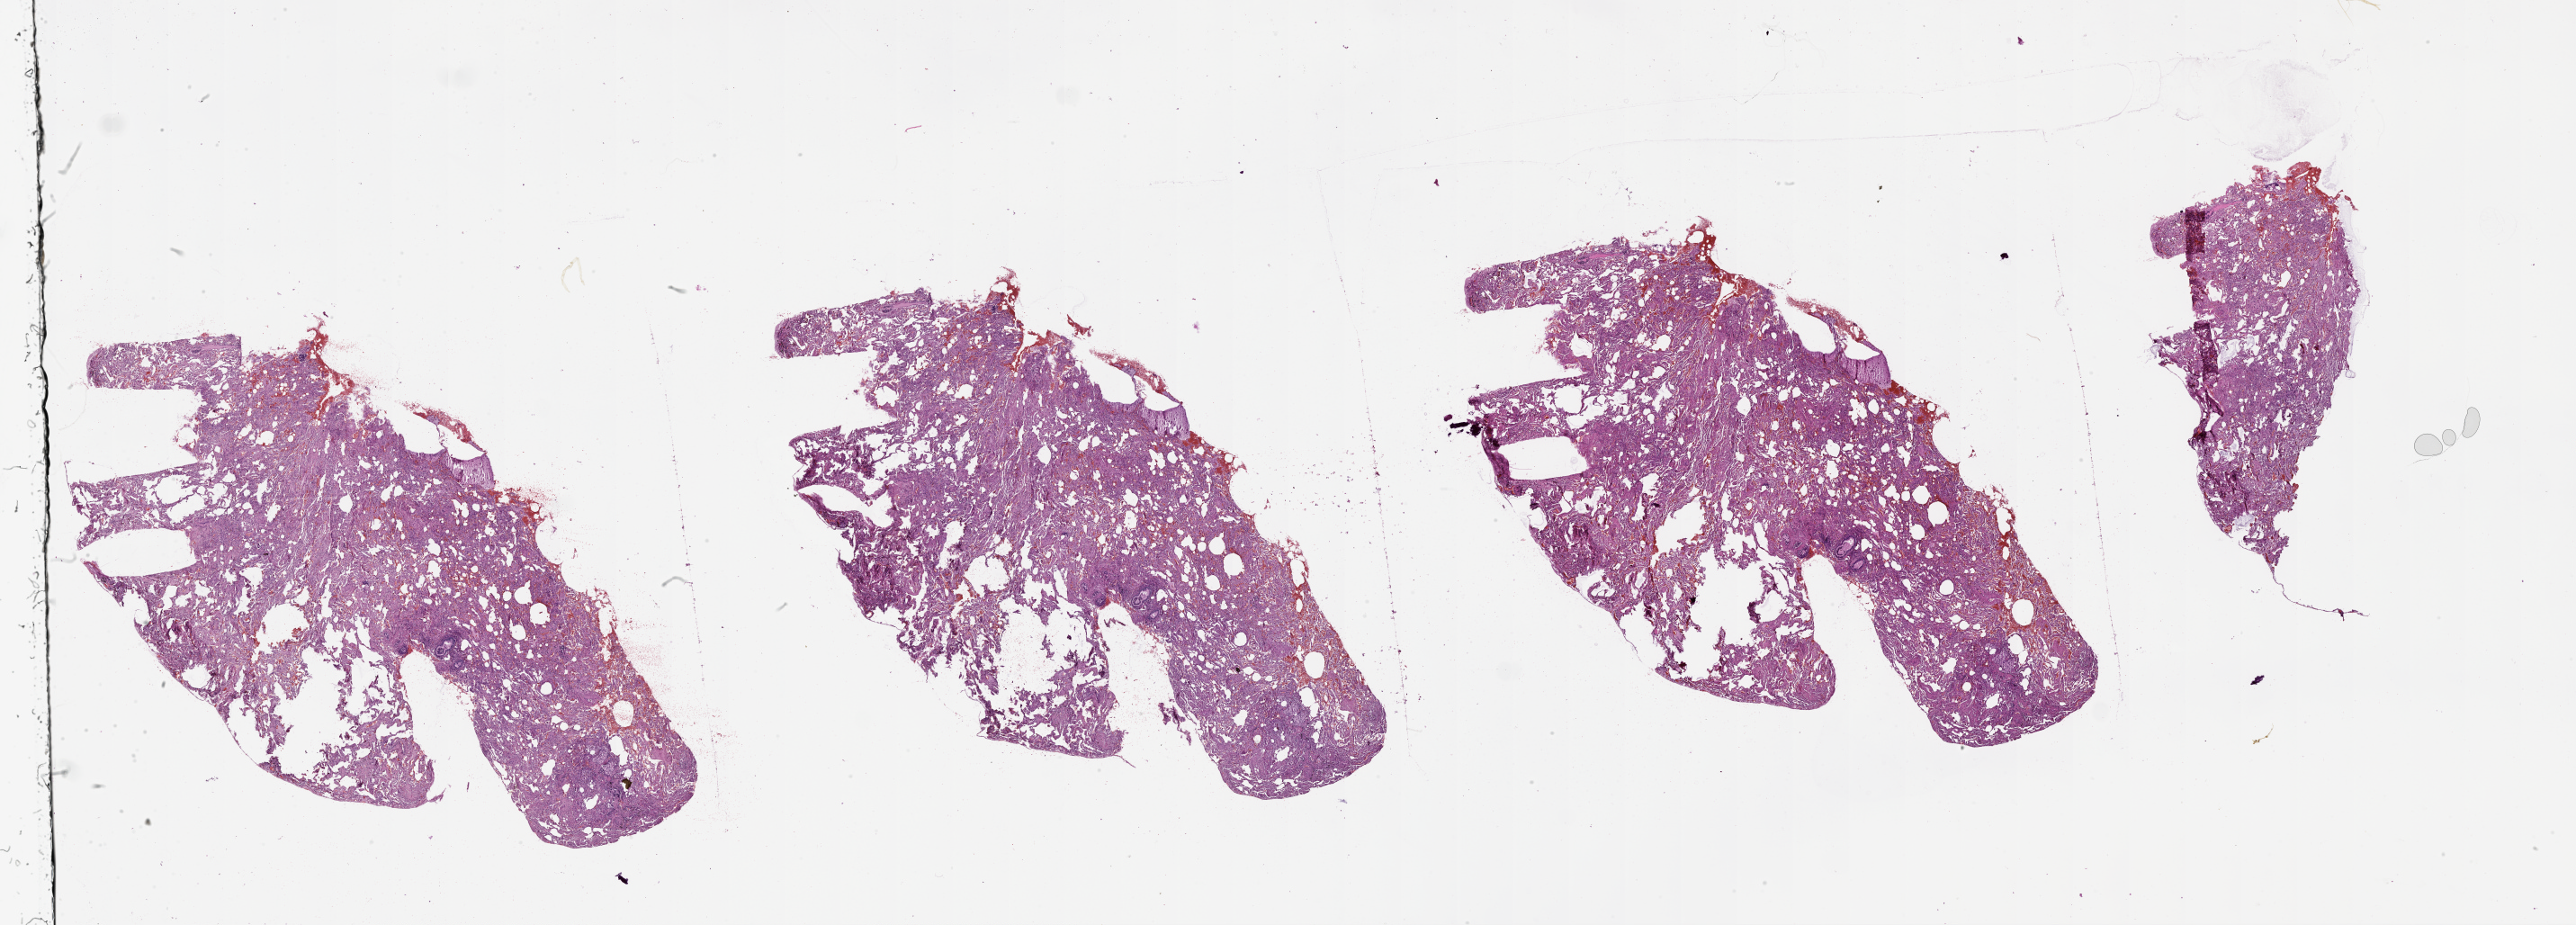
Digitized Hematoxylin and eosin (H&E) stained tissue section (whole slide), shown as a low-resolution overview of the whole scanned area (about 46.1 x 16.6 mm), normal (non-tumour) tissue sample, lung. Male, 53 y/o.
This section: normal (non-tumour) tissue from the same patient. Patient diagnosis (cohort enrolment): squamous cell carcinoma (lung).